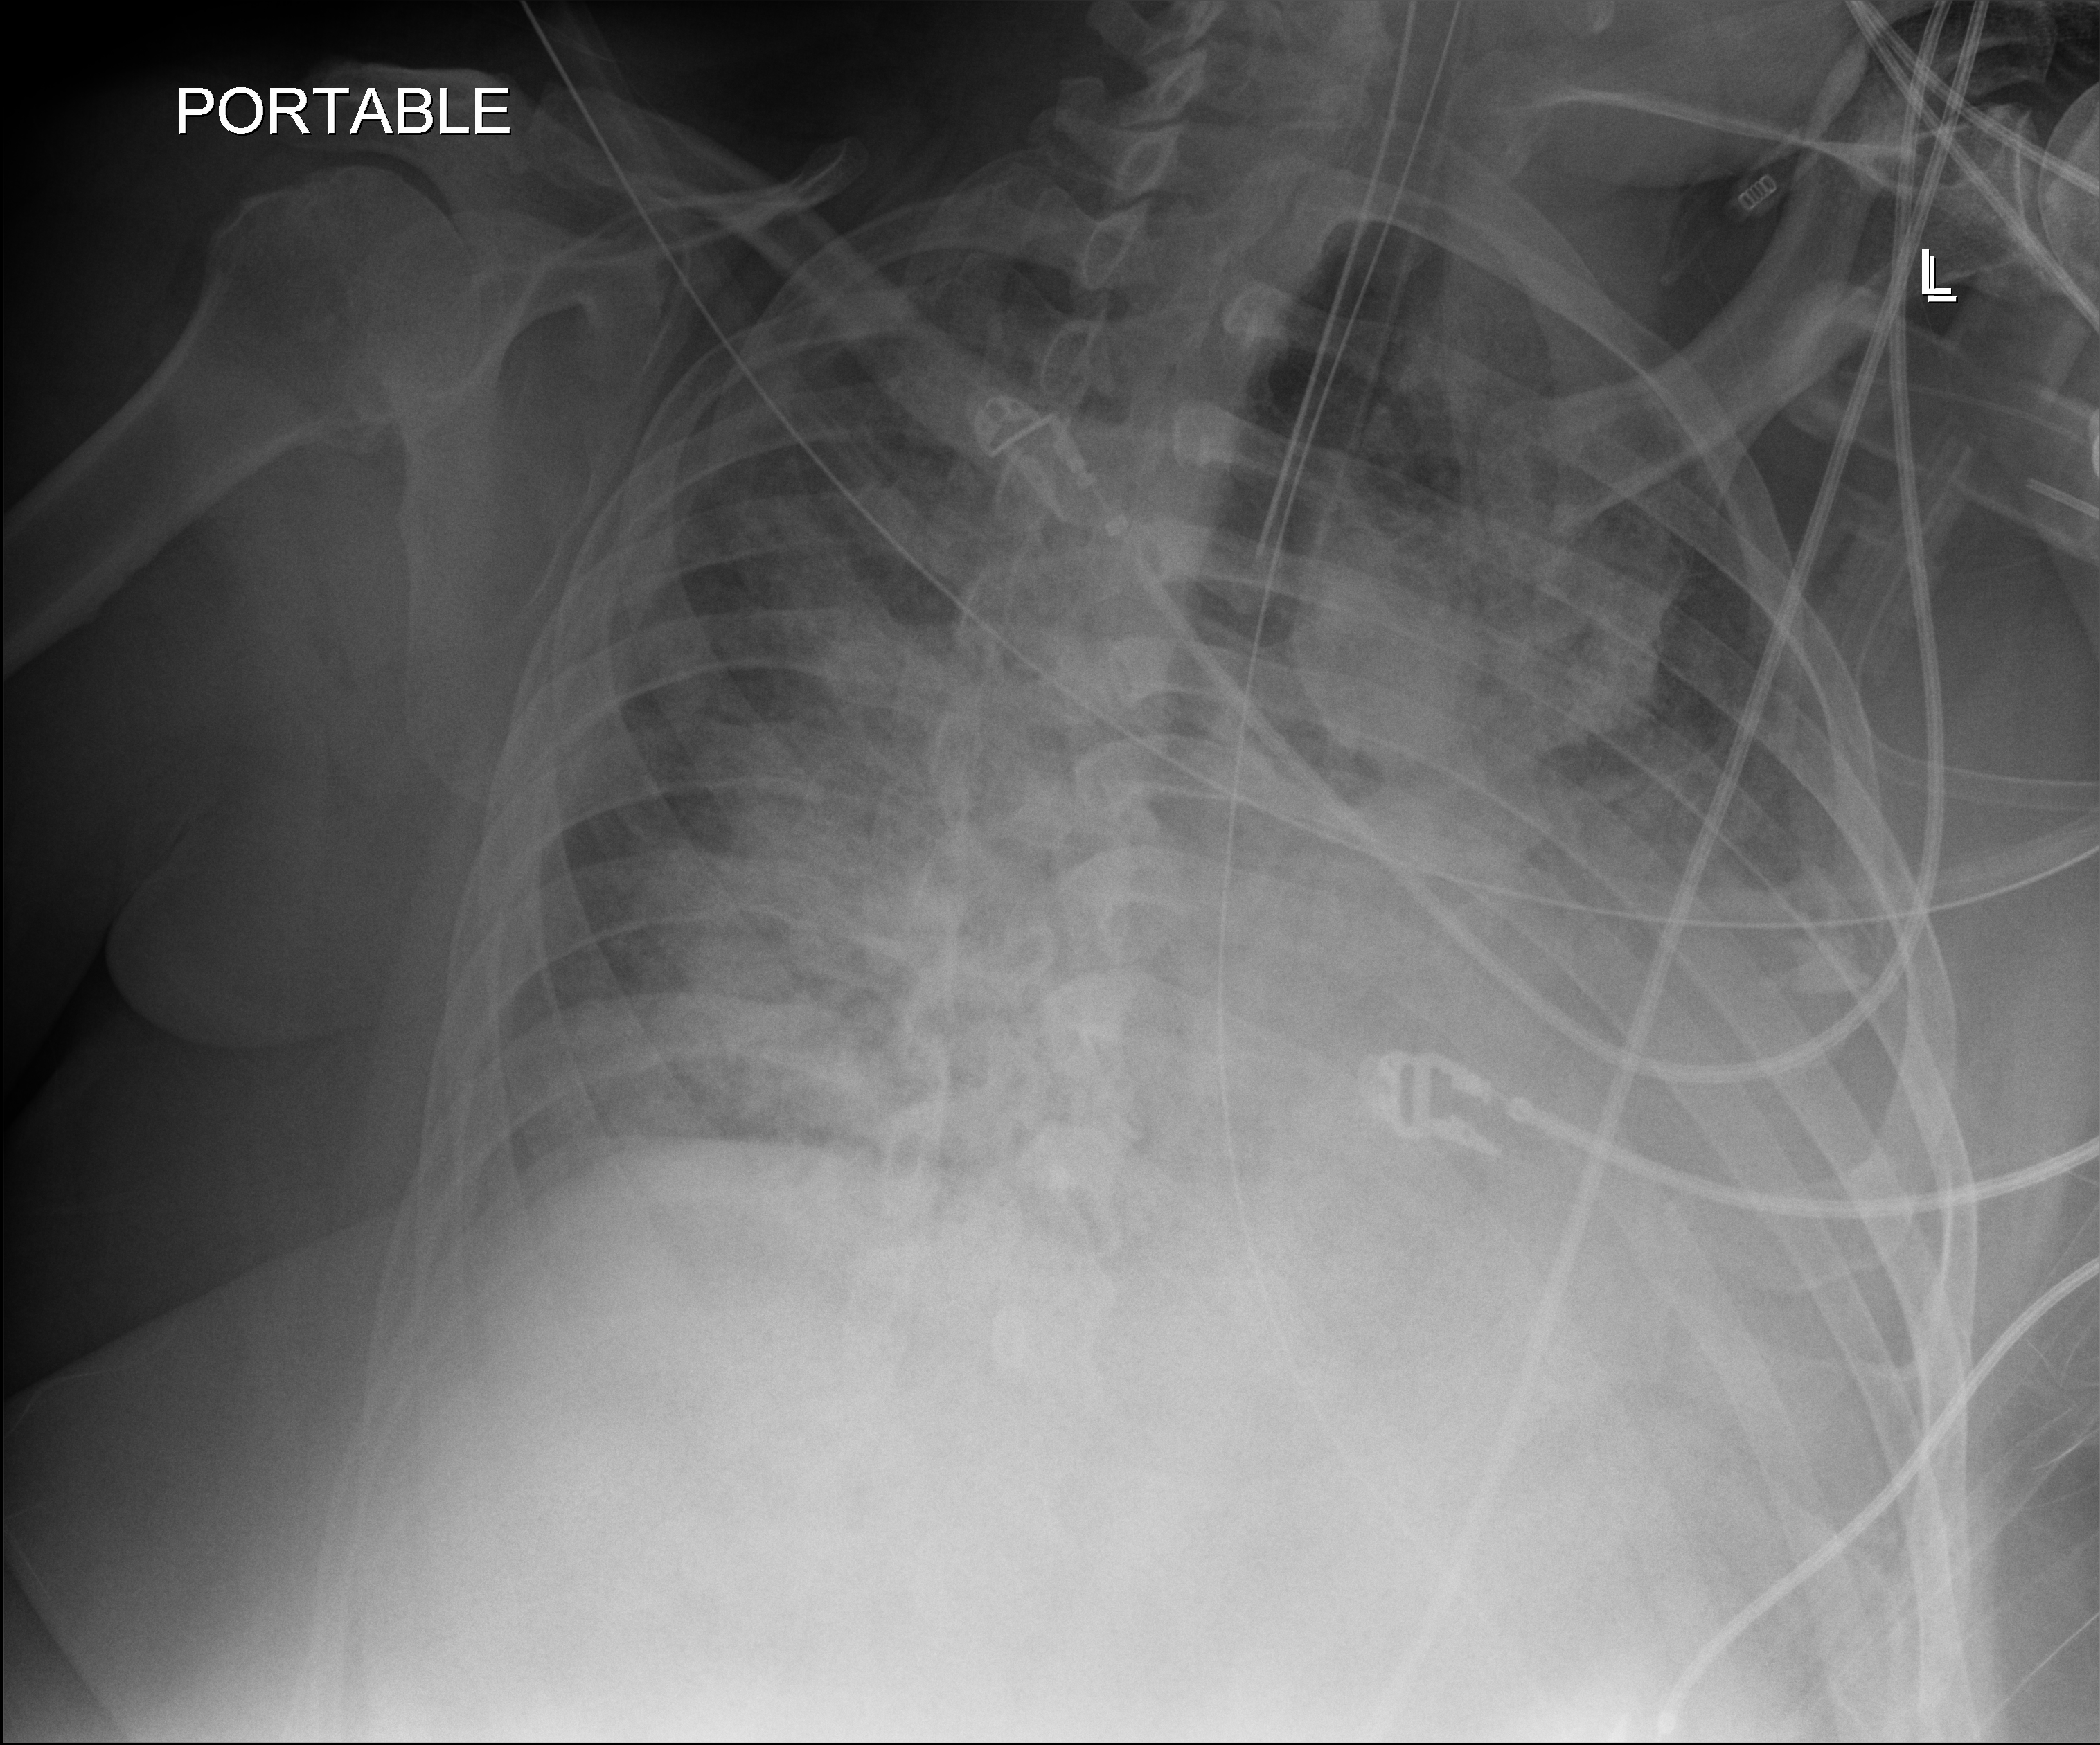
Portable chest radiograph. Patient hospitalised with COVID-19; male, aged 18–59 years.
Hospital-stay facts (about this admission, not read from this image; timing relative to this image not recorded):
- mechanically ventilated during this hospital stay: yes
- admitted to intensive care during this hospital stay: yes
- hypertension (admission record): yes